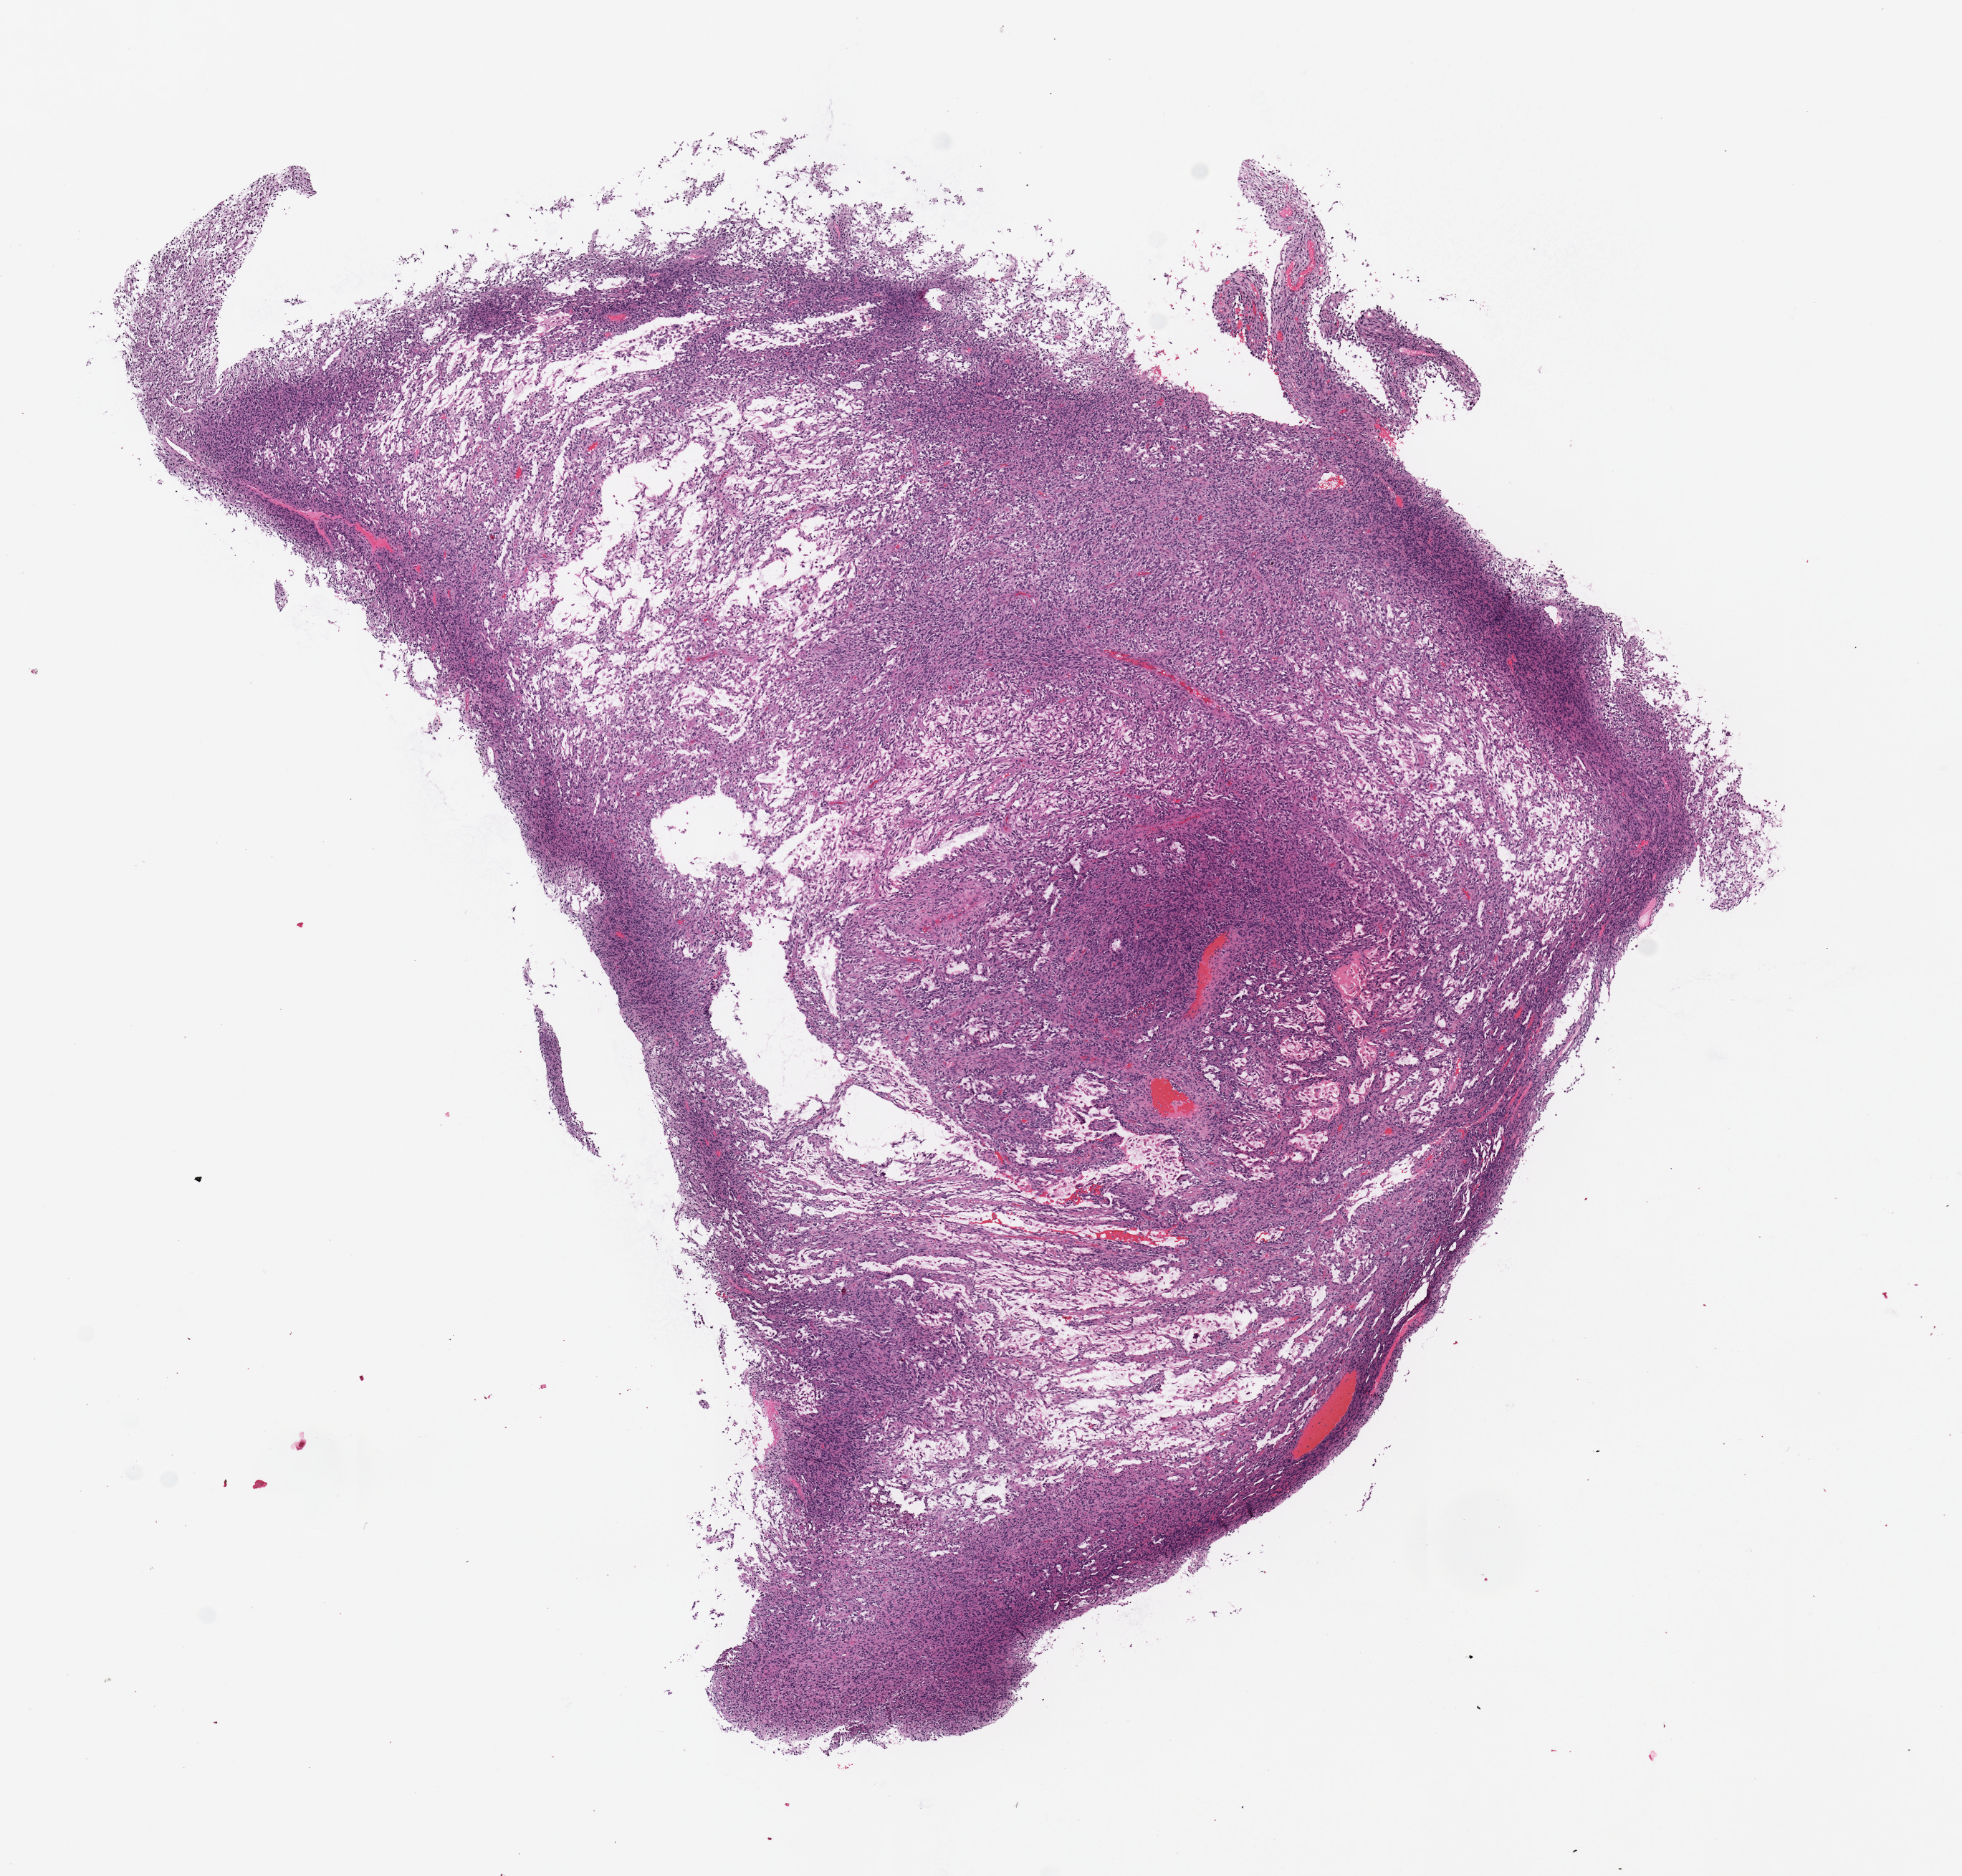
H&E-stained whole-slide image, whole scanned area (about 10.8 x 10.4 mm) shown as a low-resolution overview. Tumour tissue sample. Patient: male, age 78 years.
Patient diagnosis (cohort enrolment): sarcoma (site not recorded at cohort level). Primary tumour site (as recorded): upper extremity.